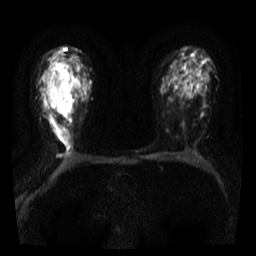
Breast MRI, one axial slice. Position 23 of 36 along the scan axis. Diffusion-weighted series; image 2 of 4 stored at this slice position (different b-values; order by instance number). 3 T. 5 mm slice thickness. 256 × 256 image matrix, field of view 300 × 300 mm. Female patient.
Annotated regions visible in this slice (expert manual segmentation):
- tumour on diffusion-weighted imaging: bounding box <53,73,71,105> (left, top, right, bottom; pixels)